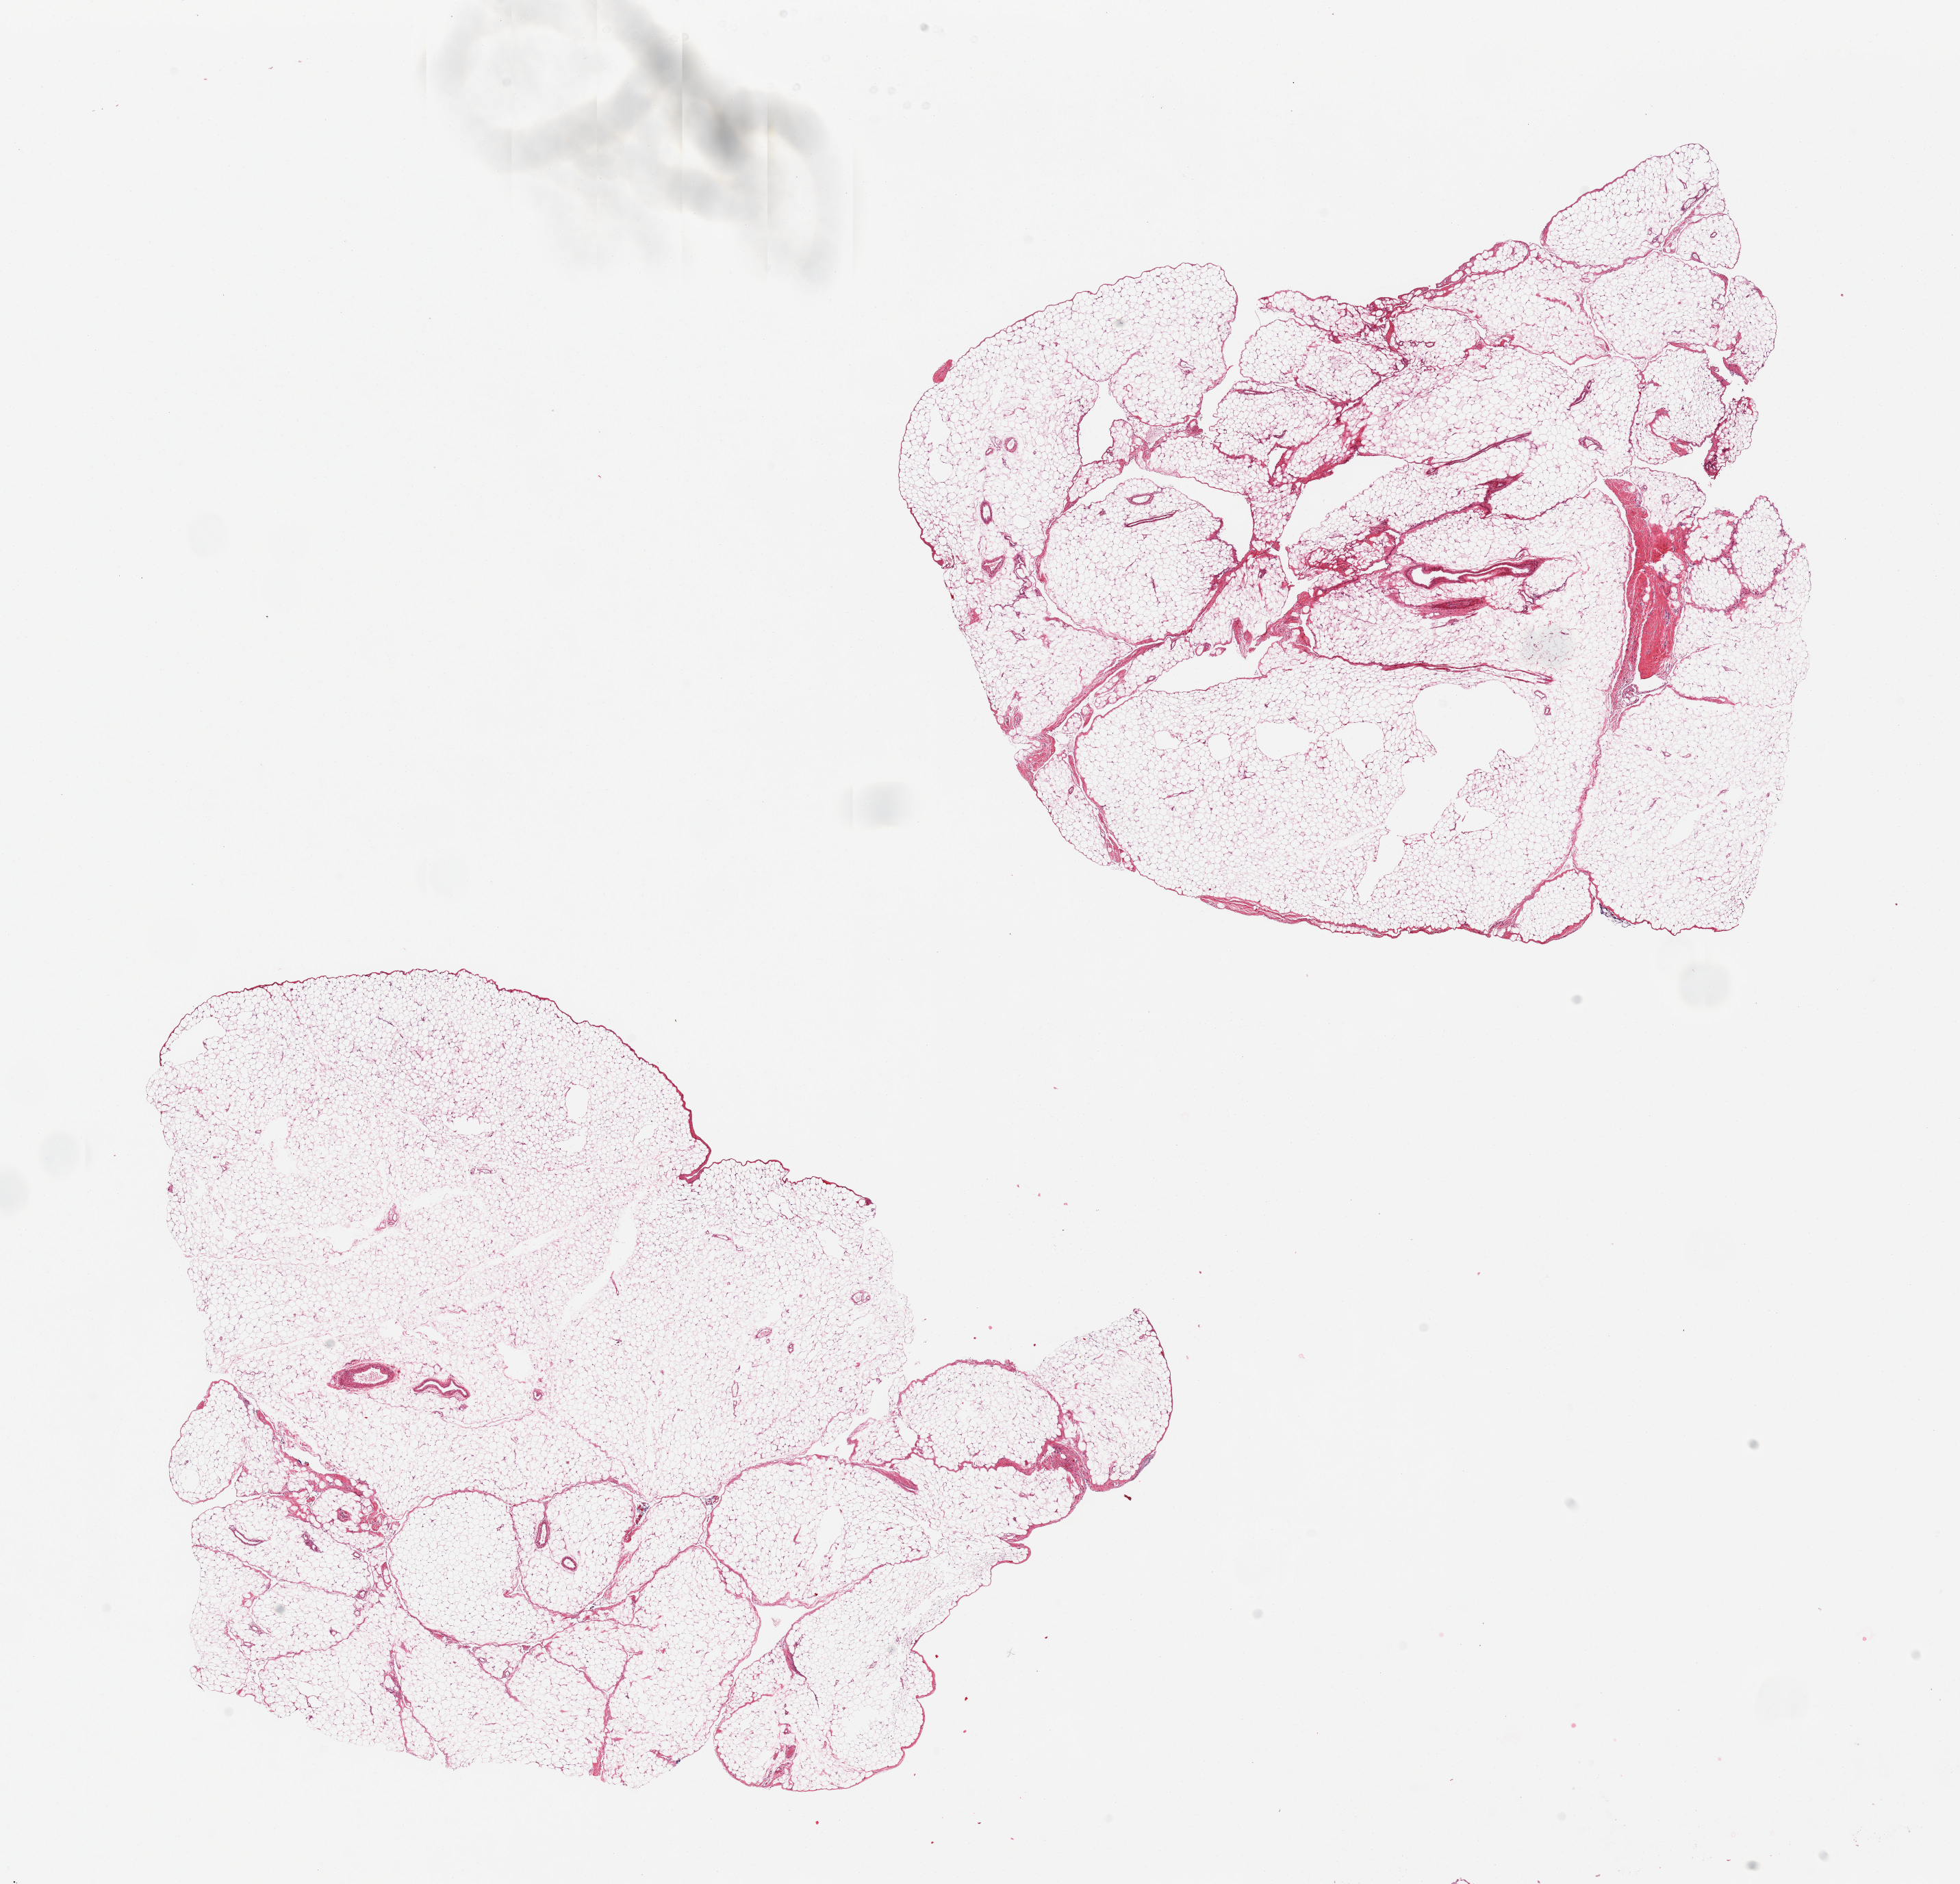
Digitized H&E-stained section — a low-resolution overview of the entire scanned area, about 22.6 x 21.8 mm (from a 20x scan); PAXgene-fixed paraffin-embedded (PFPE) section; sampled site (target tissue): omentum; donor tissue sample. Donor: female.
- reviewer comment on this tissue sample: 2 pieces